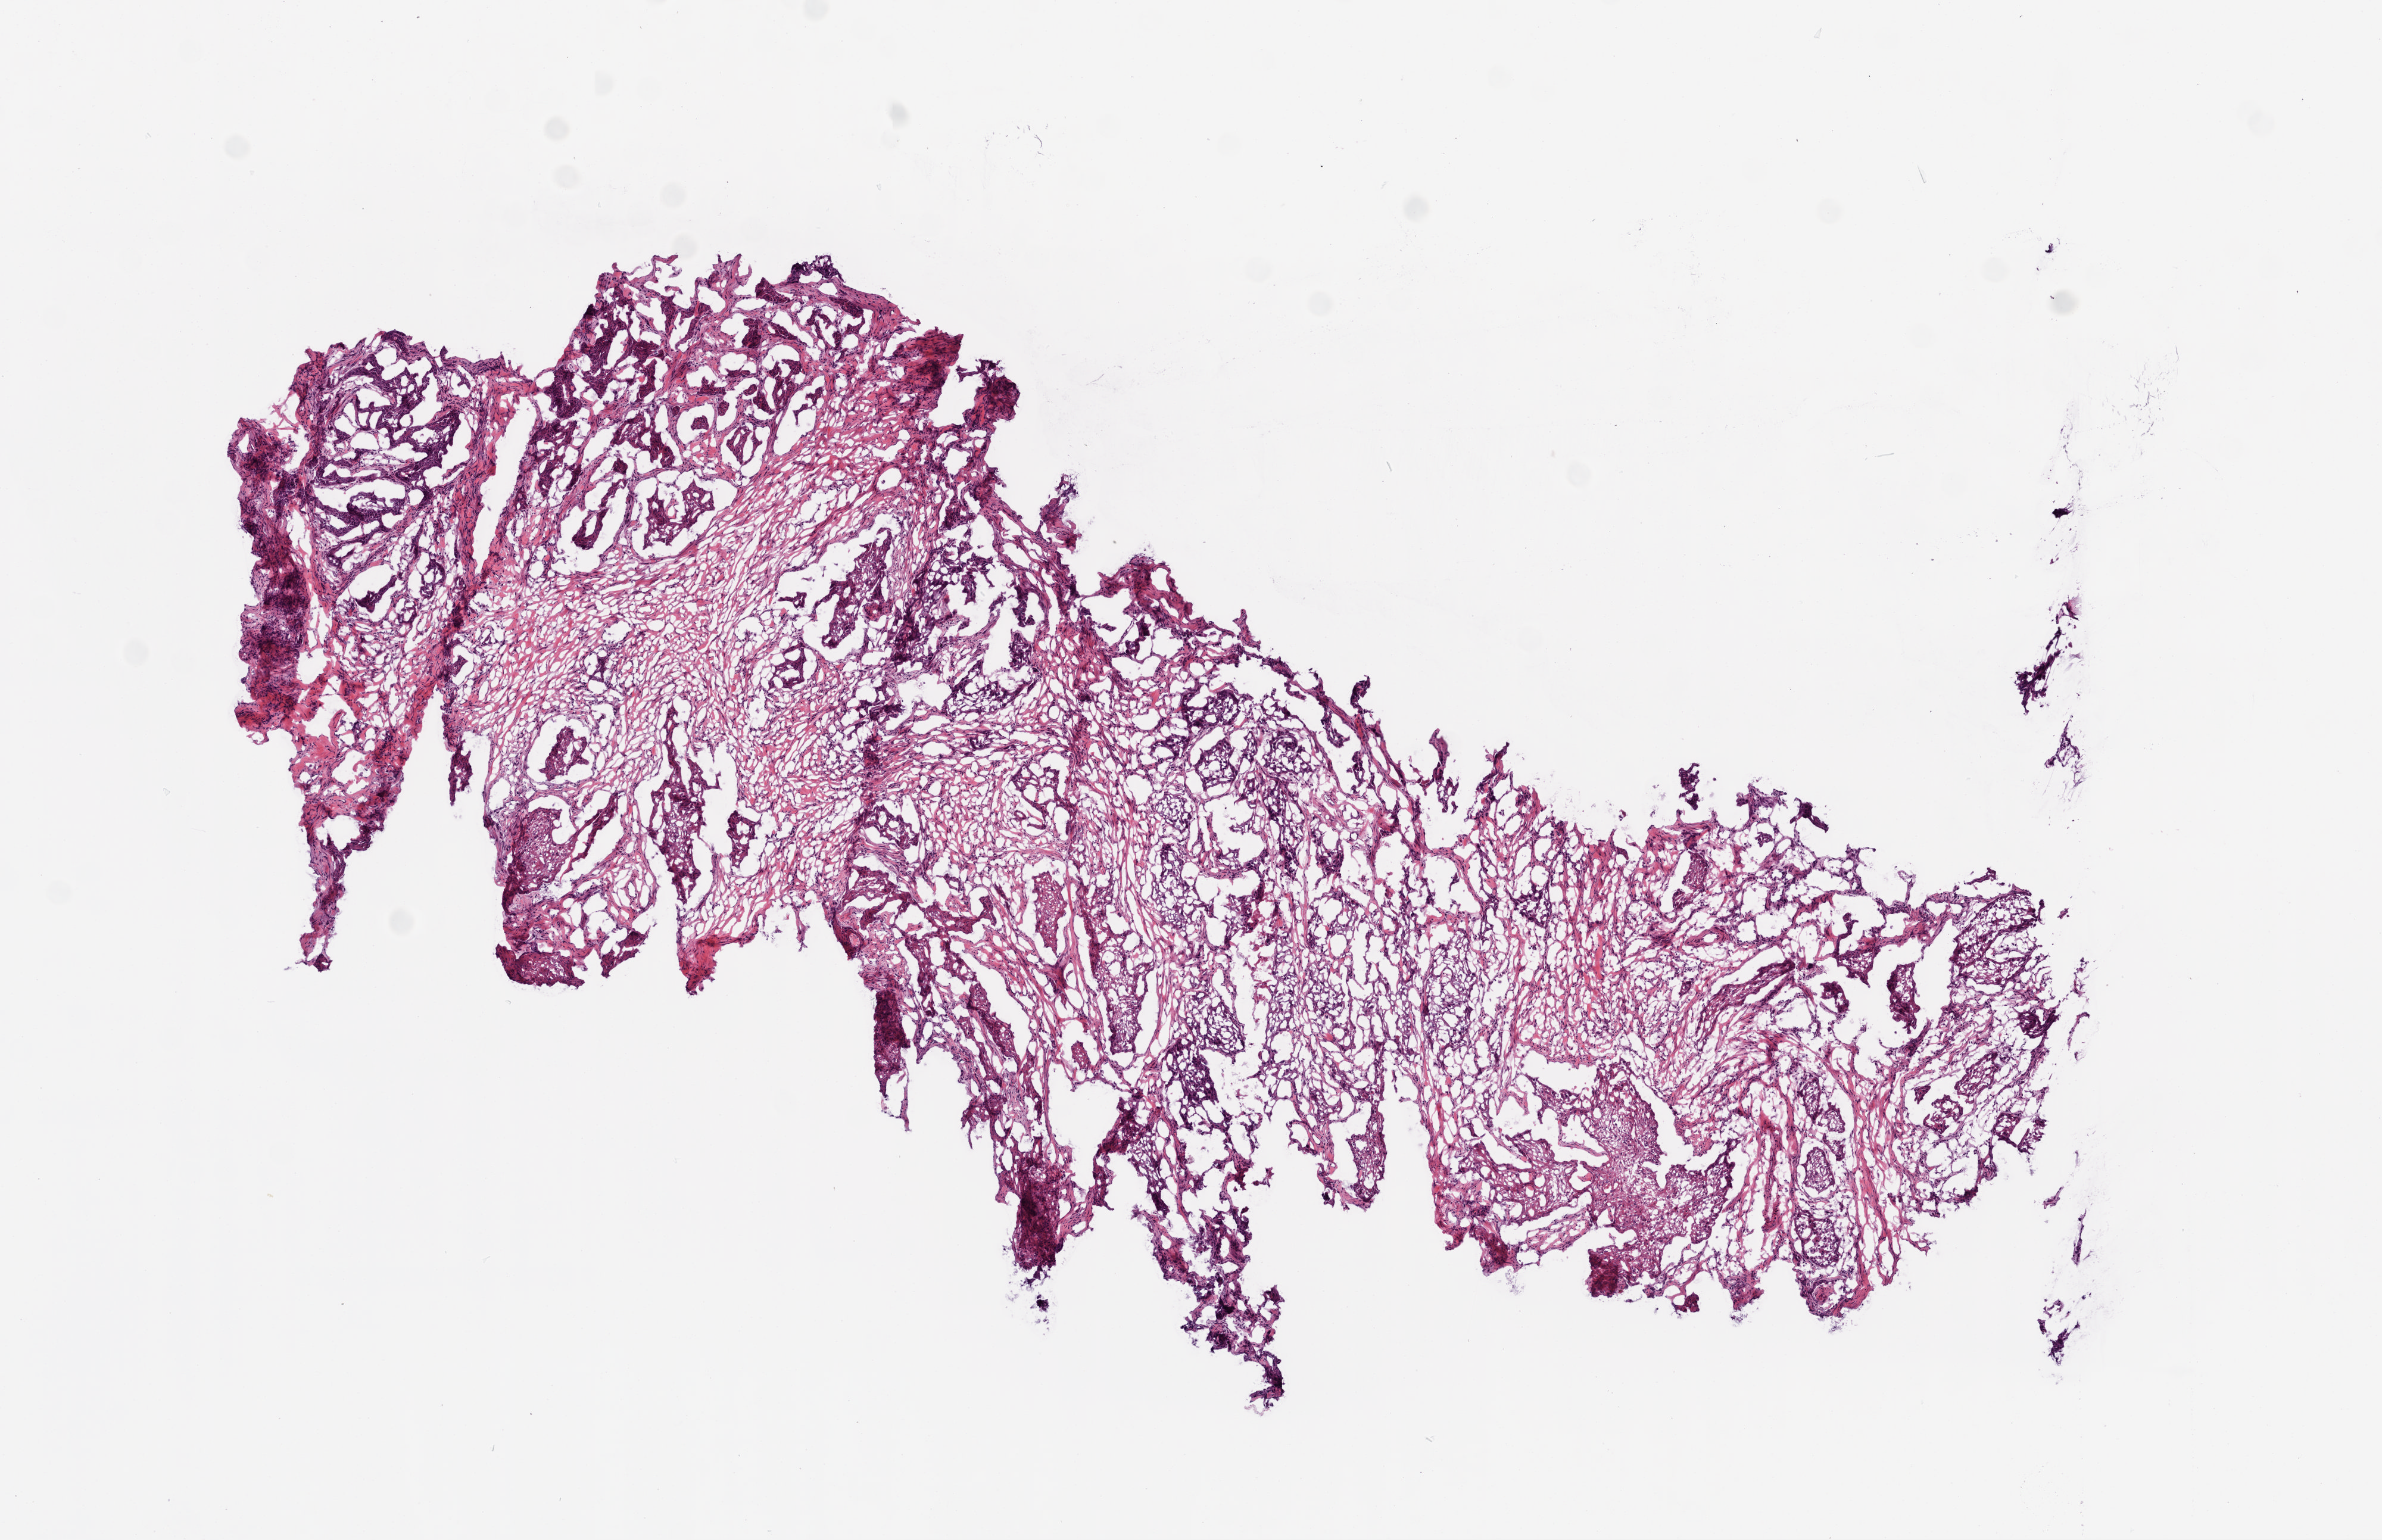
Digitized H&E-stained tissue section (whole slide) — low-resolution overview of the scanned area, about 8.0 x 5.2 mm; frozen section from the top of the tissue portion; primary tumour sample from the head and neck. Patient: male, age at initial diagnosis 80 years. Histologic grade: G2 (moderately differentiated). Pathologist review of this section (percent, as recorded): tumour cells 70%, tumour nuclei 80%, normal cells 0%, stromal cells 30%, necrosis 0%.
• diagnosis: Squamous cell carcinoma, NOS (larynx, NOS)
• AJCC pathologic stage: IVA